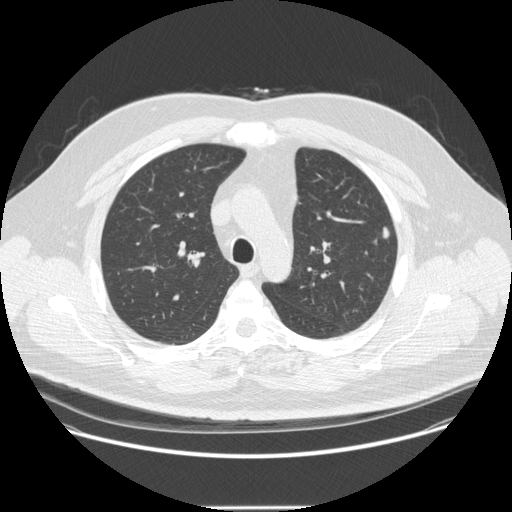
Axial slice from a low-dose chest CT screening exam; second annual screen; lung window (W 1500 / L -600 HU); 1.25 mm slice thickness; standard (soft-tissue) reconstruction kernel (STANDARD); 120 kVp; 512 × 512 image matrix, field of view 410 × 410 mm. Male participant, aged 55 years at enrolment. Former smoker at enrolment.
Lesion marked by an expert reader, box from (x=373, y=225) to (x=406, y=250) px. The screening reader recorded 2 non-calcified nodules or masses ≥4 mm on this exam (left upper lobe, left upper lobe); which of them this box marks is not recorded. Official screen result: positive, other. Lung cancer was diagnosed 60 days after this screen: adenocarcinoma, NOS, left upper lobe, moderately differentiated (G2), stage IA (AJCC 6th edition), 9 mm at pathology.